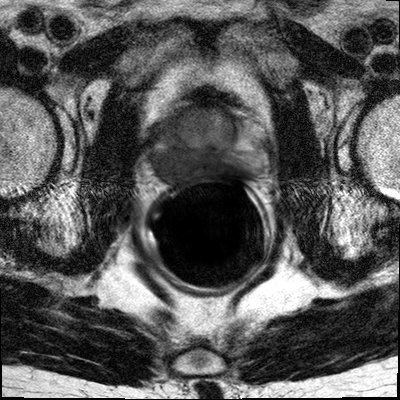
Multiparametric prostate MRI examination; 3 images, each a single mid-volume slice chosen by position (not for content). Treatment context recorded for this patient: No Surgery, treatment with Degarelix.
Image 1: T2-weighted axial slice, slice 17 of 32, 3 mm slice thickness.
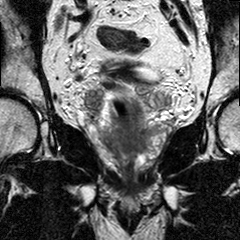
Image 2: T2-weighted coronal slice, series "T2W_TSE_COR", slice 13 of 24.
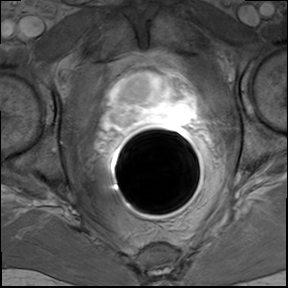
Image 3: DCE (dynamic gadolinium-enhanced) axial slice, series "AX BLISS_GAD_8", slice 17 of 32, dynamic phase 5 of 8.
Radiologist's MRI report for this examination:
There is a large tumor seen within the right posterior and posterior lateral peripheral zone of the prostate in the mid 3rd, with extension into the apex and the base, involving on some levels nearly the entire right peripheral zone including the lateral horn and part of the adjacent central gland paramedian right, with extension to the fibromuscular band anteriorly. The tumor extends also to the left and involves the posterior and posterior lateral left peripheral zone. Total tumor extension on some levels from 4 o'clock to 11 o'clock. On the right the tumor bulges towards the right neurovascular bundle. However, no more mass seen within the neurovascular bundle / or beyond the pseudo capsule on either side. There is no evidence of manifest vesicle infiltration however beginning at infiltration of the seminal vesicle base cannot be excluded. There is a prominent middle lobe protruding into the bladder neck. Due to marked motion artifact evaluation for pelvic lymphadenopathy not possible; CT examination recommended for assessment of the lymph nodes. IMPRESSION: Large bilateral tumor involving predominantly the right peripheral zone and right central gland; and to a lesser extent the left peripheral zone, with dominant mass in the mid-third, and extension to apex and base (maximal diameter in the axial plane is 4.5 cm). There is bulging towards the right neurovascular bundle at the mid third level however no tumor mass is seen within the neurovascular bundle on either side. No definite seminal vesicle infiltration. Beginning infiltration of the seminal vesicle base cannot be excluded. CT pelvis examination recommended for assessment of lymphadenopathy. Obtained images are not diagnostic due to marked motion artifact.

Biopsy pathology report for this patient (as recorded):
PROSTATE BIOPSIES: 1. RIGHT PZ: PROSTATIC ADENOCARCINOMA, GLEASON SCORE 4+3=7/10, PRESENT IN 2 CORES AND APPROXIMATELY 70% OF TISSUE SUBMITTED. PERINEURAL INVASION IS PRESENT. 2. RIGHT PZ/TZ: PROSTATIC ADENOCARCINOMA, GLEASON SCORE 4+3=7/10, PRESENT IN 3 CORES AND APPROXIMATELY 70% OF TISSUE SUBMITTED. PERINEURAL INVASION IS PRESENT. 3. RIGHT APEX: PROSTATIC ADENOCARCINOMA, GLEASON SCORE 4+3=7/10, PRESENT IN 4 CORES AND APPROXIMATELY 80% OF TISSUE SUBMITTED. 4. LEFT PZ: PROSTATIC ADENOCARCINOMA, GLEASON SCORE 3+3=6/10, PRESENT IN 1 CORE AND APPROXIMATELY 40% OF TISSUE SUBMITTED. 5. LEFT PZ/TZ: PROSTATIC ADENOCARCINOMA, GLEASON SCORE 3+4=7/10, PRESENT IN 2 CORES AND APPROXIMATELY 50% OF TISSUE SUBMITTED. PERINEURAL INVASION IS PRESENT. 6. LEFT APEX: PROSTATIC ADENOCARCINOMA, GLEASON SCORE 4+3=7/10, PRESENT IN 2 CORES AND APPROXIMATELY 60% OF TISSUE SUBMITTED. PERINEURAL INVASION IS PRESENT.